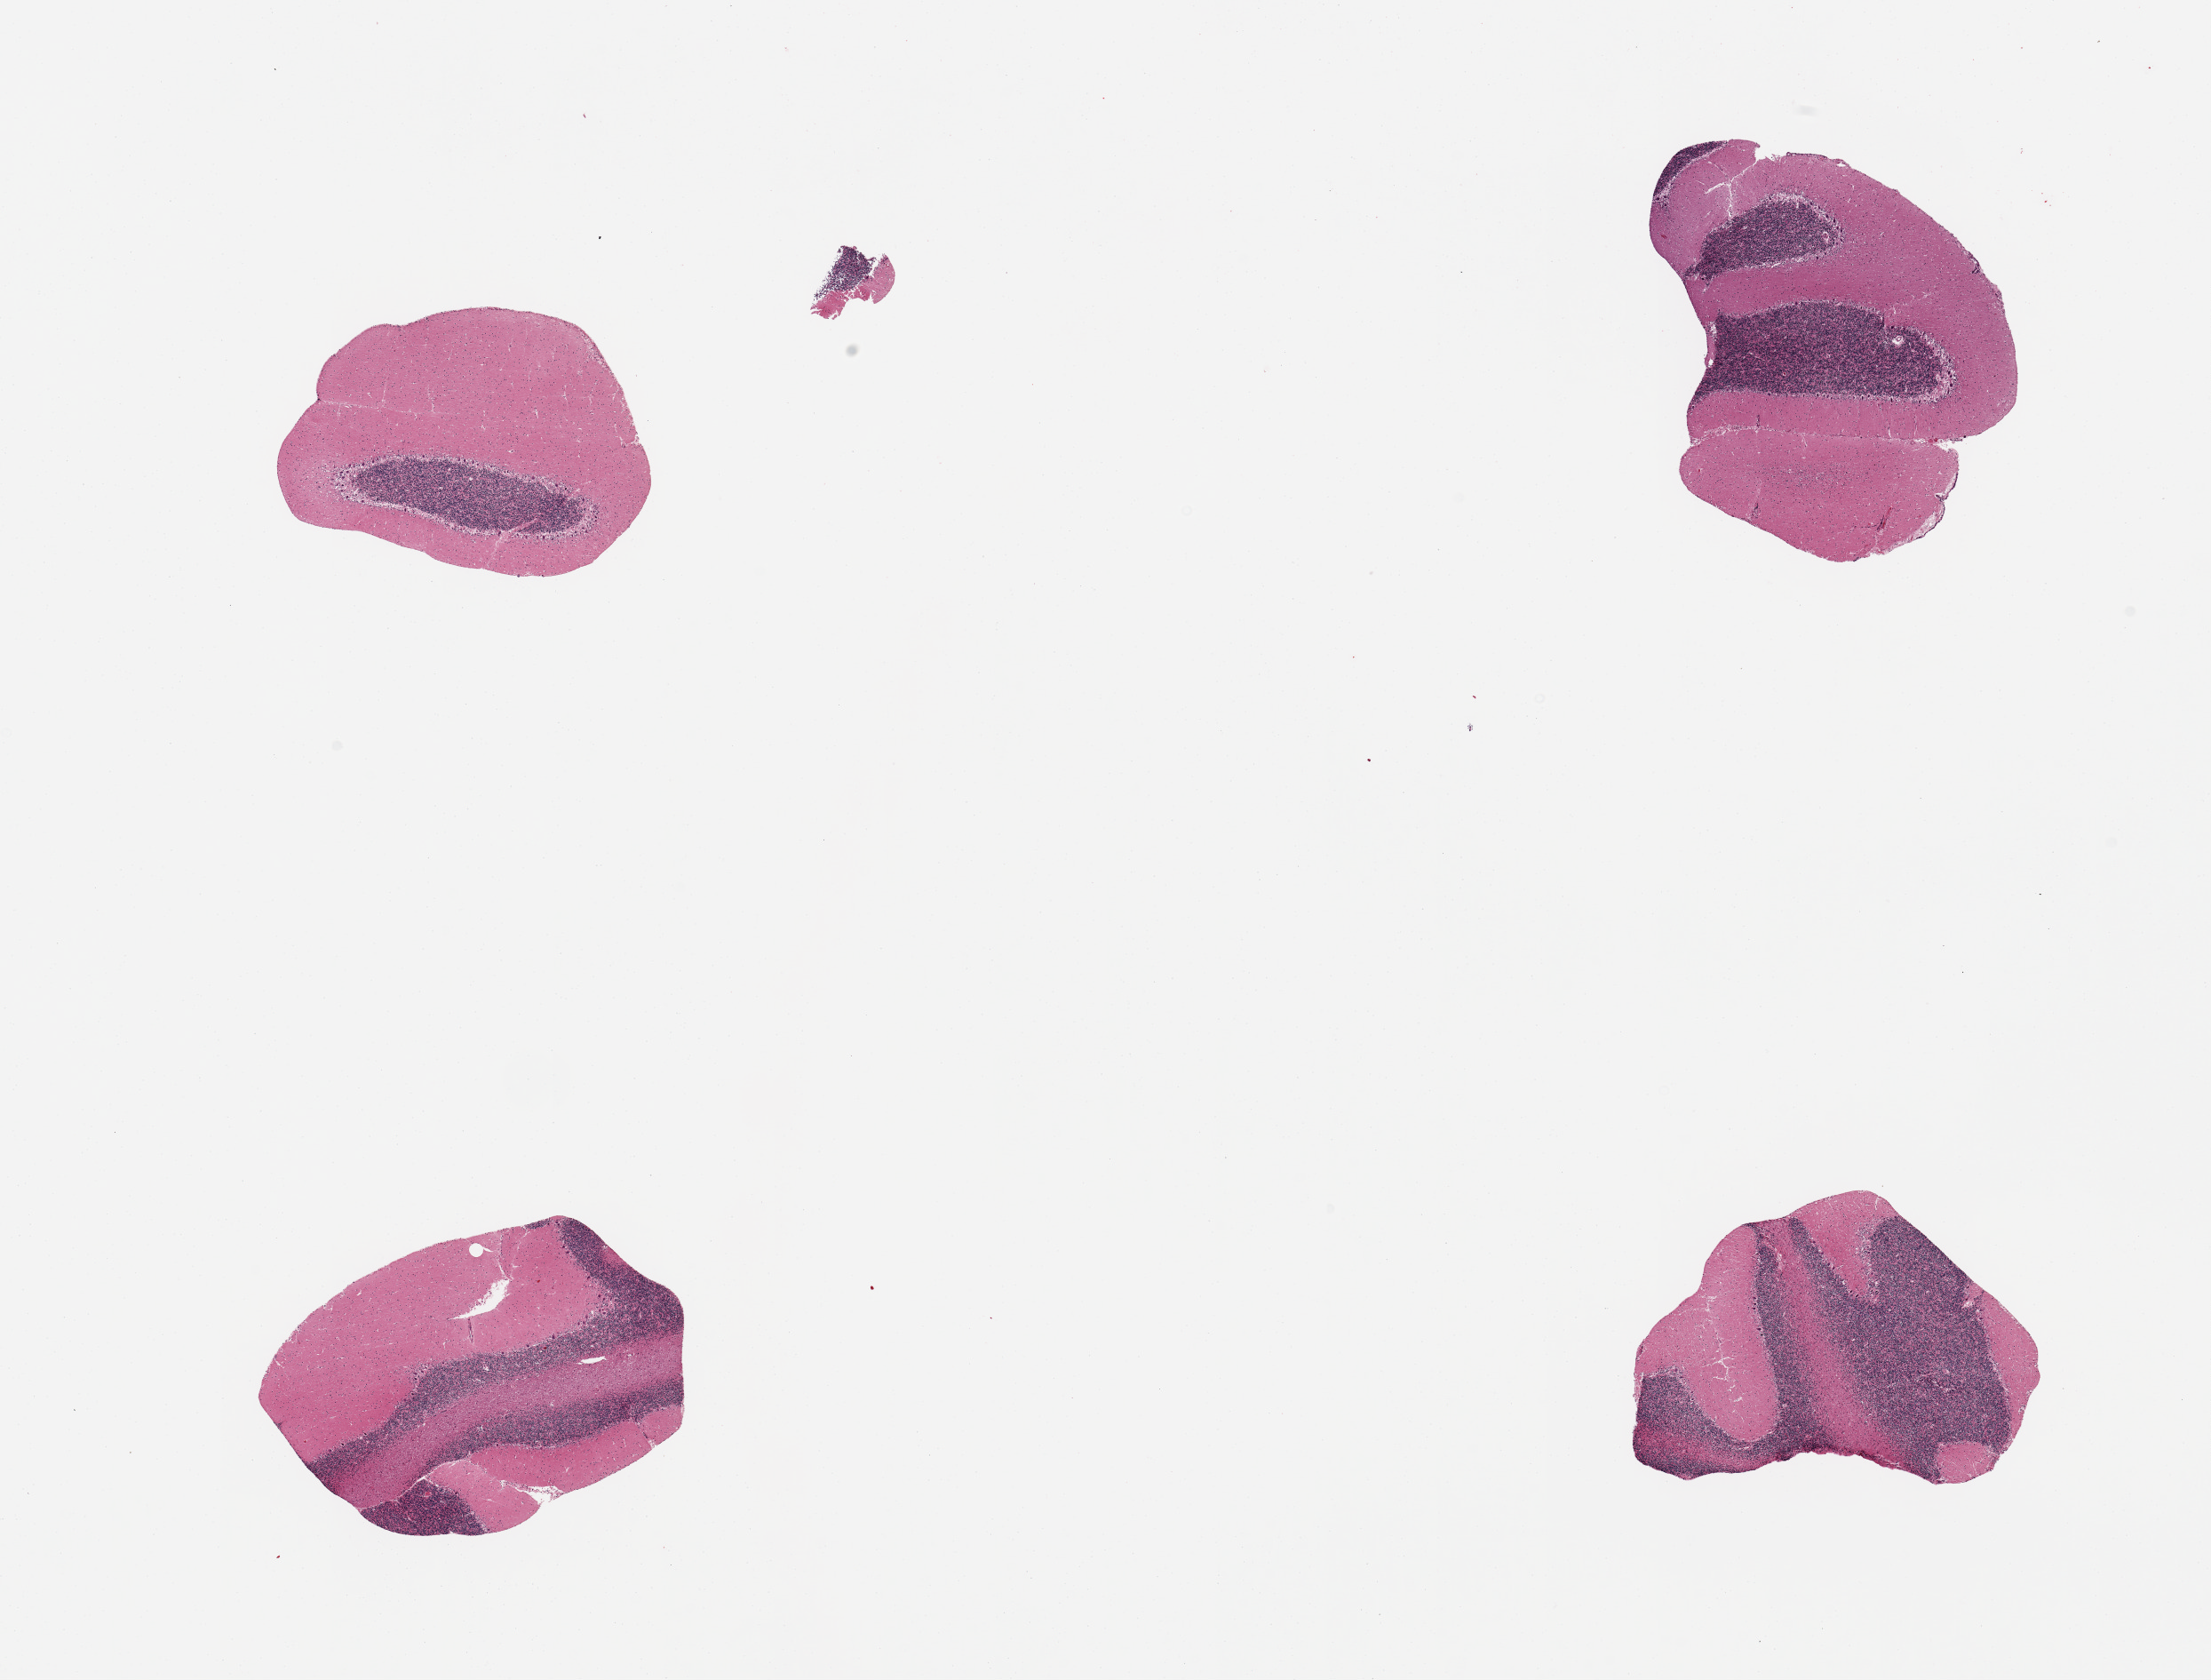
Whole-slide image, hematoxylin and eosin (H&E) stain, brightfield, whole scanned area (about 19.7 x 15.0 mm, from a 20x scan) shown as a low-resolution overview. PAXgene-fixed paraffin-embedded (PFPE) section. Section of cerebellum (target tissue). Donor tissue sample. Male donor.
Review note (as recorded): 4 pieces, no abnormalities.